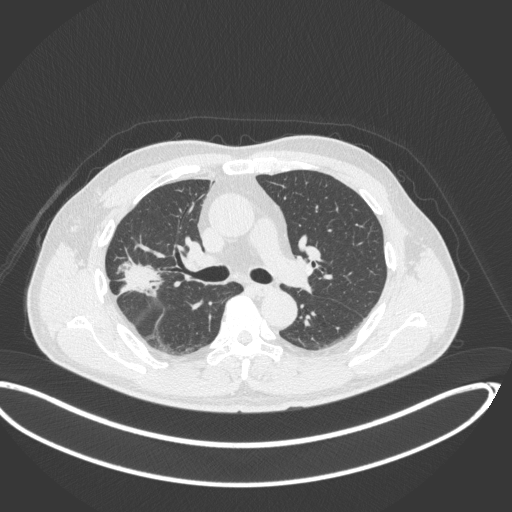
Chest CT, one axial slice; position 210 of 341 along the scan axis; lung window (W 1500 / L -600 HU); 1 mm slice thickness; 512 × 512 image matrix. Patient: male, 63 years. Case-level facts recorded for this patient, not image findings: clinical TNM (as recorded): T1c N0 M0; histopathological grade: G2-3.
Structures marked on this image (bounding box drawn by a radiologist):
- lung tumour (recorded histology: adenocarcinoma): bounding box <112,251,165,302> (left, top, right, bottom; pixels)